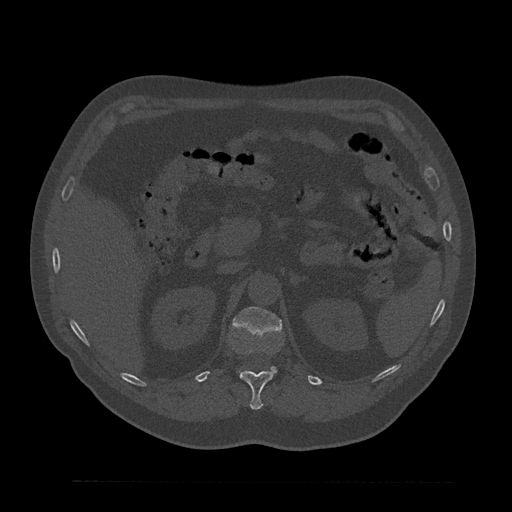
CT including the spine, one axial slice; slice 205 of 797 in the series (ordered by position); 120 kVp; bone window (W 1800 / L 400 HU); 0.5 mm slice thickness; 512 × 512 image matrix, field of view 430 × 430 mm. Patient: male, 61 years. Case-level facts recorded for this patient, not image findings: primary cancer: prostate.
Annotated regions visible in this slice (semi-automatic segmentation, software-assisted and operator-edited):
- L1 vertebra: bounding box [x1, y1, x2, y2] px = [233, 307, 282, 374]
- T12 vertebra: [239, 349, 273, 410]